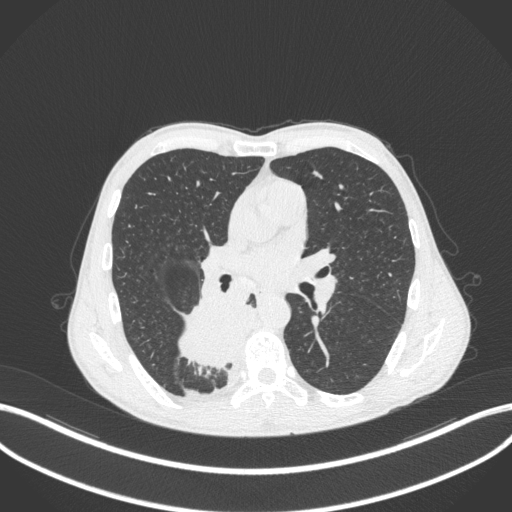
Chest CT, one axial slice. Position 204 of 371 along the scan axis. Reconstruction kernel B31f. 120 kVp. Lung window (W 1500 / L -600 HU). 512 × 512 image matrix. Patient: male, 58 years. Case-level facts recorded for this patient, not image findings: clinical TNM (as recorded): T3 N1 M1.
Outlined on this slice (rectangle marked by the reading radiologist):
- lung tumour (recorded histology: squamous cell carcinoma): bounding box [x1, y1, x2, y2] px = [171, 294, 258, 372]